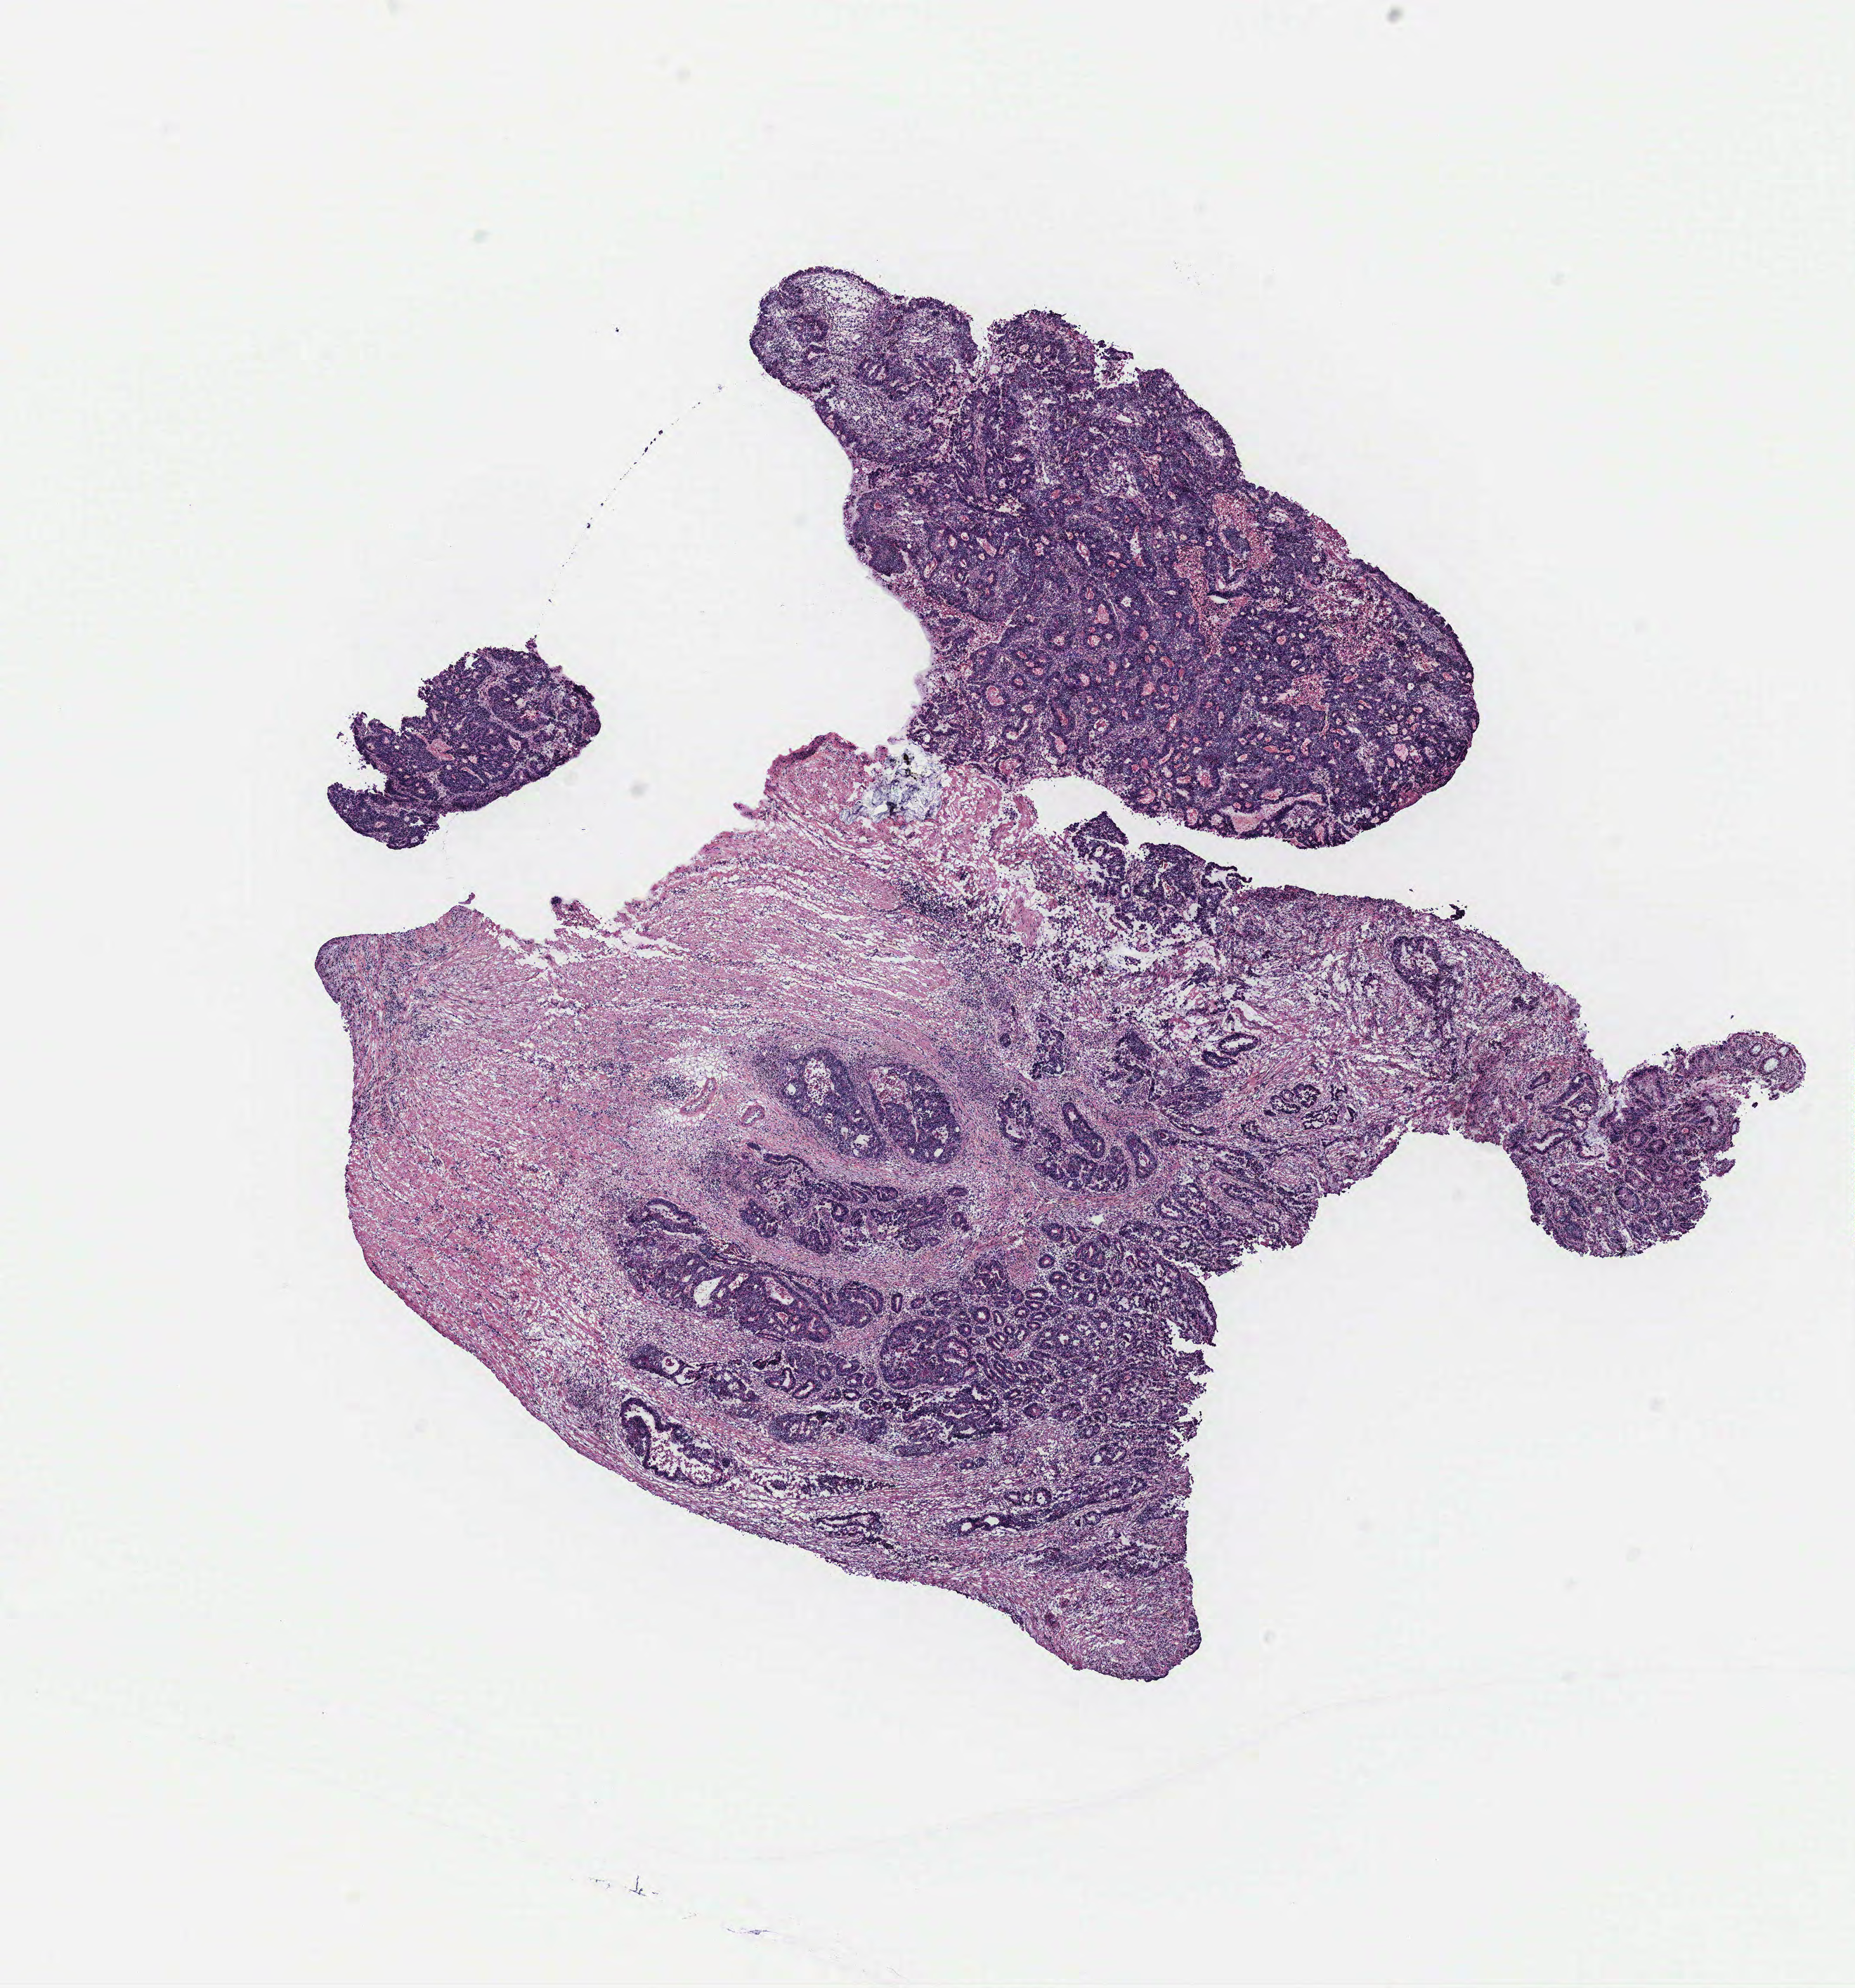
Whole-slide histology image, H&E, low-resolution overview of the scanned area, about 10.6 x 11.3 mm (acquisition: 40x scan), tumour tissue sample, colon. Patient: female, age 49 years.
• patient diagnosis (cohort enrolment): colon cancer (colon)
• primary tumour site (as recorded): colon